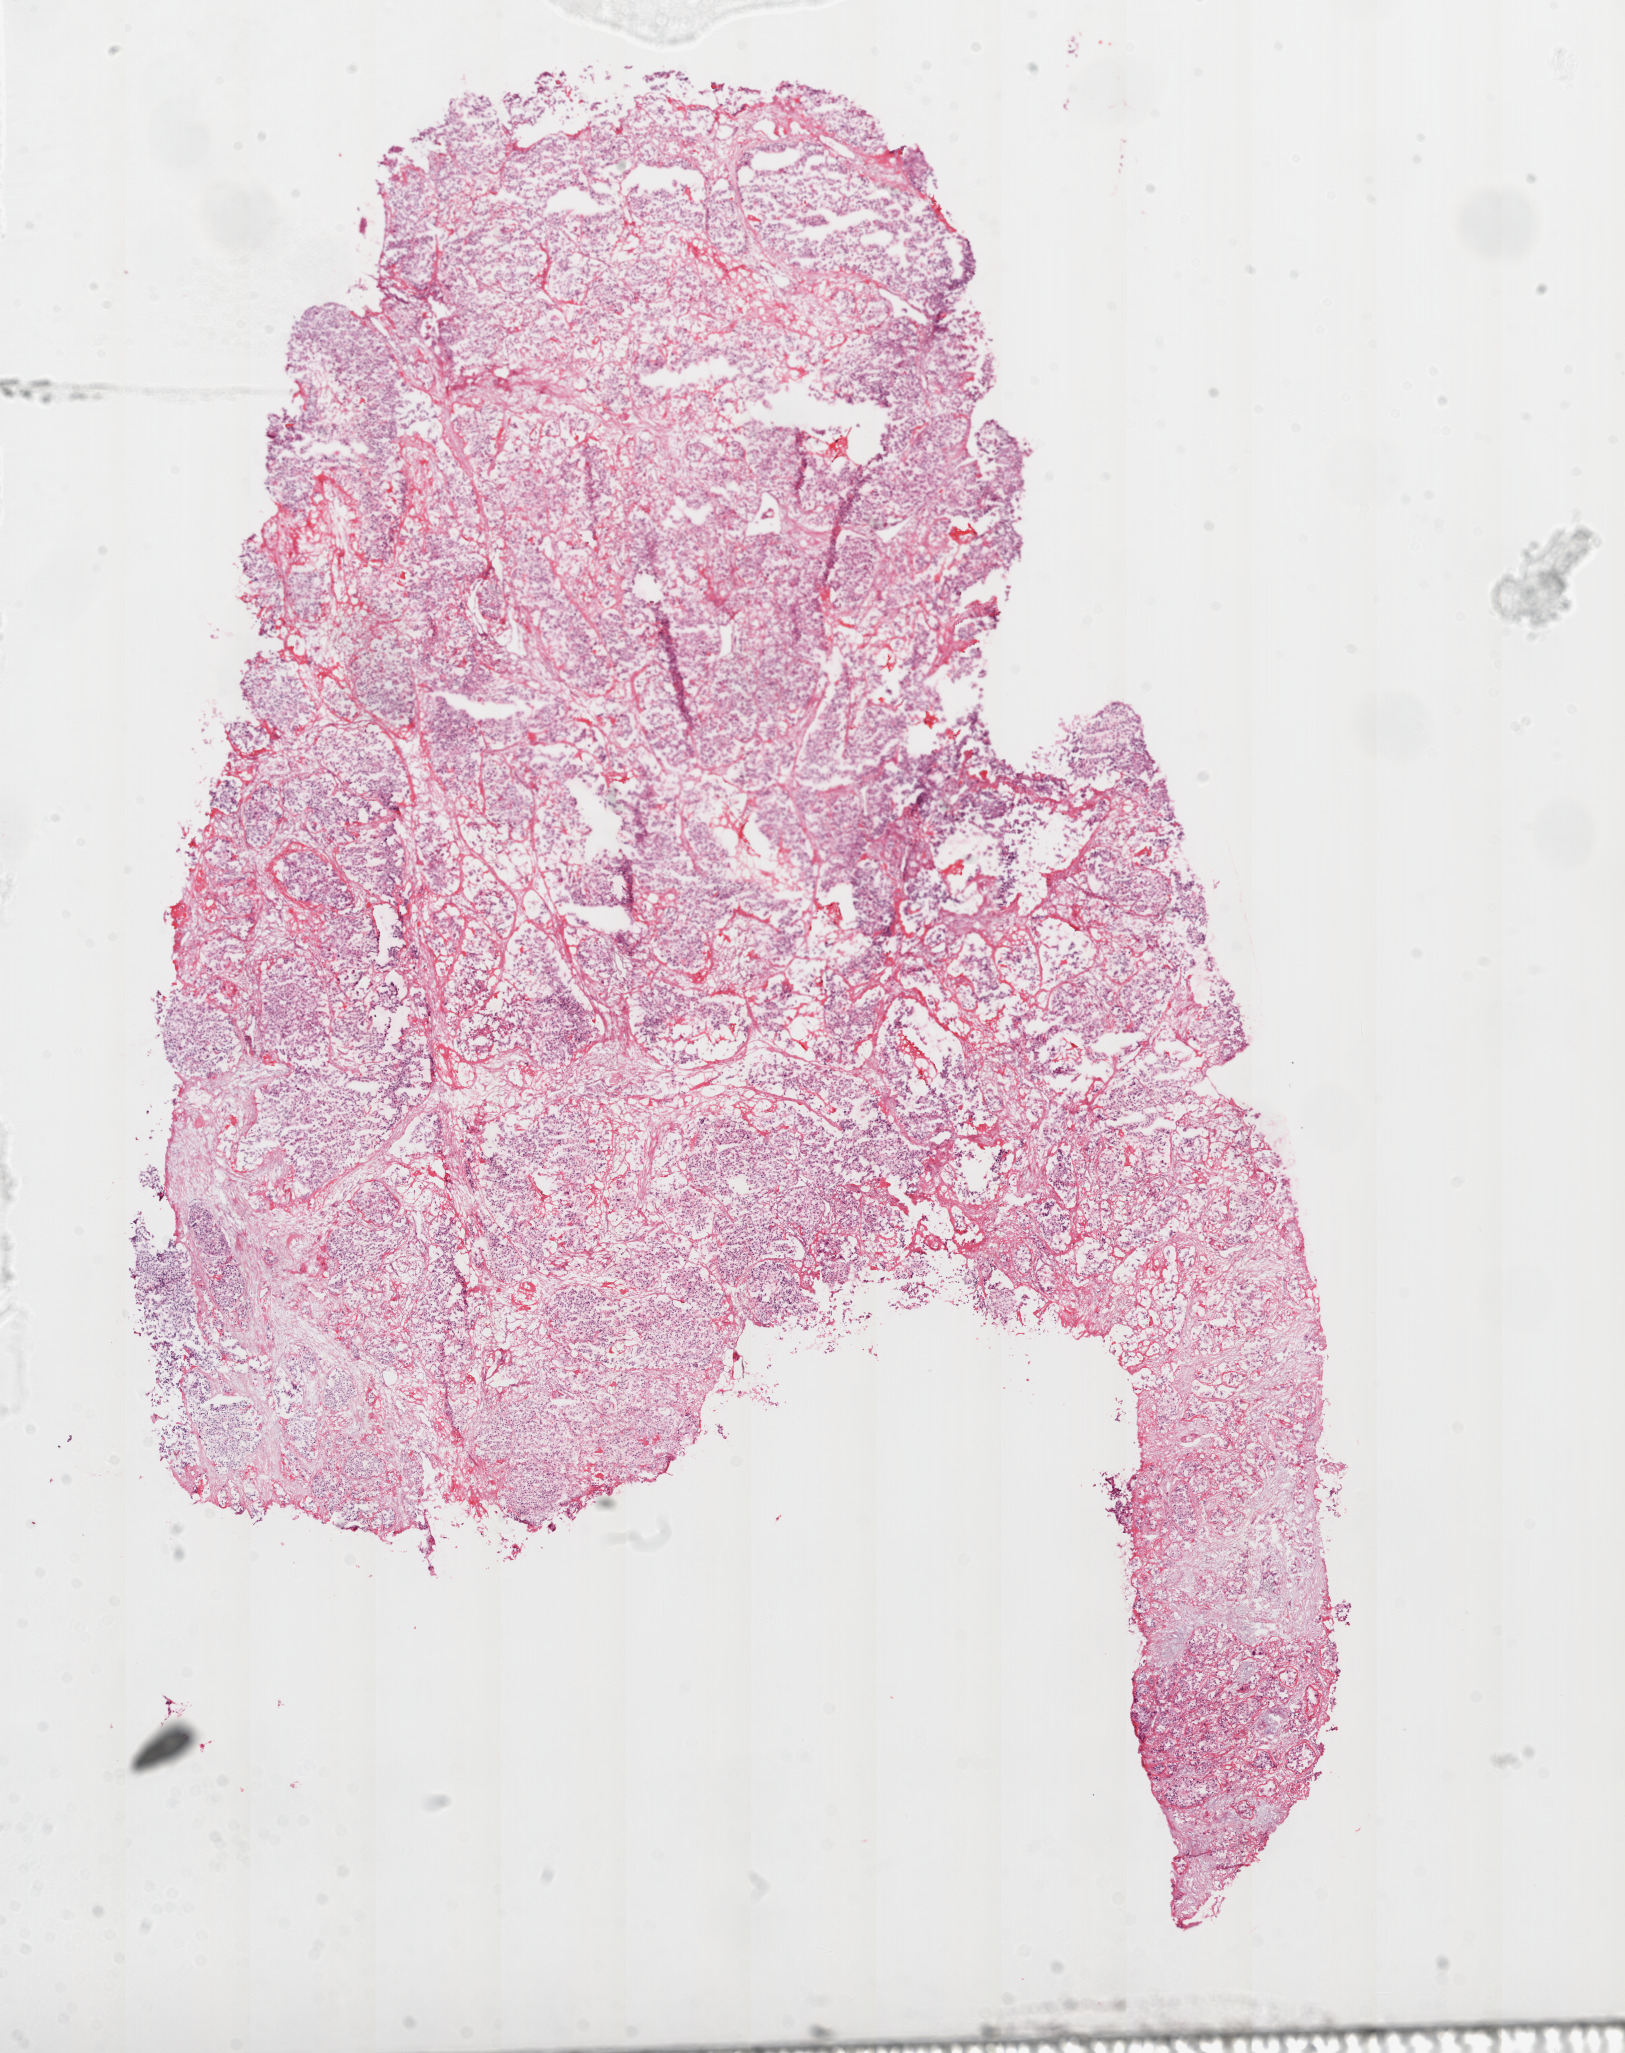
H&E whole-slide image — a low-resolution overview of the entire scanned area, about 13.0 x 16.5 mm (slide scanned at 20x), frozen section from the top of the tissue portion, sample: primary tumour, kidney. Male, age 60 years at initial diagnosis. Histologic grade: G4 (undifferentiated). Slide review estimates, as recorded: tumour cells 85%, tumour nuclei 85%, normal cells 0%, stromal cells 15%, necrosis 0%.
Laterality: right. AJCC pathologic stage: IV. Histologic diagnosis: Clear cell adenocarcinoma, NOS.